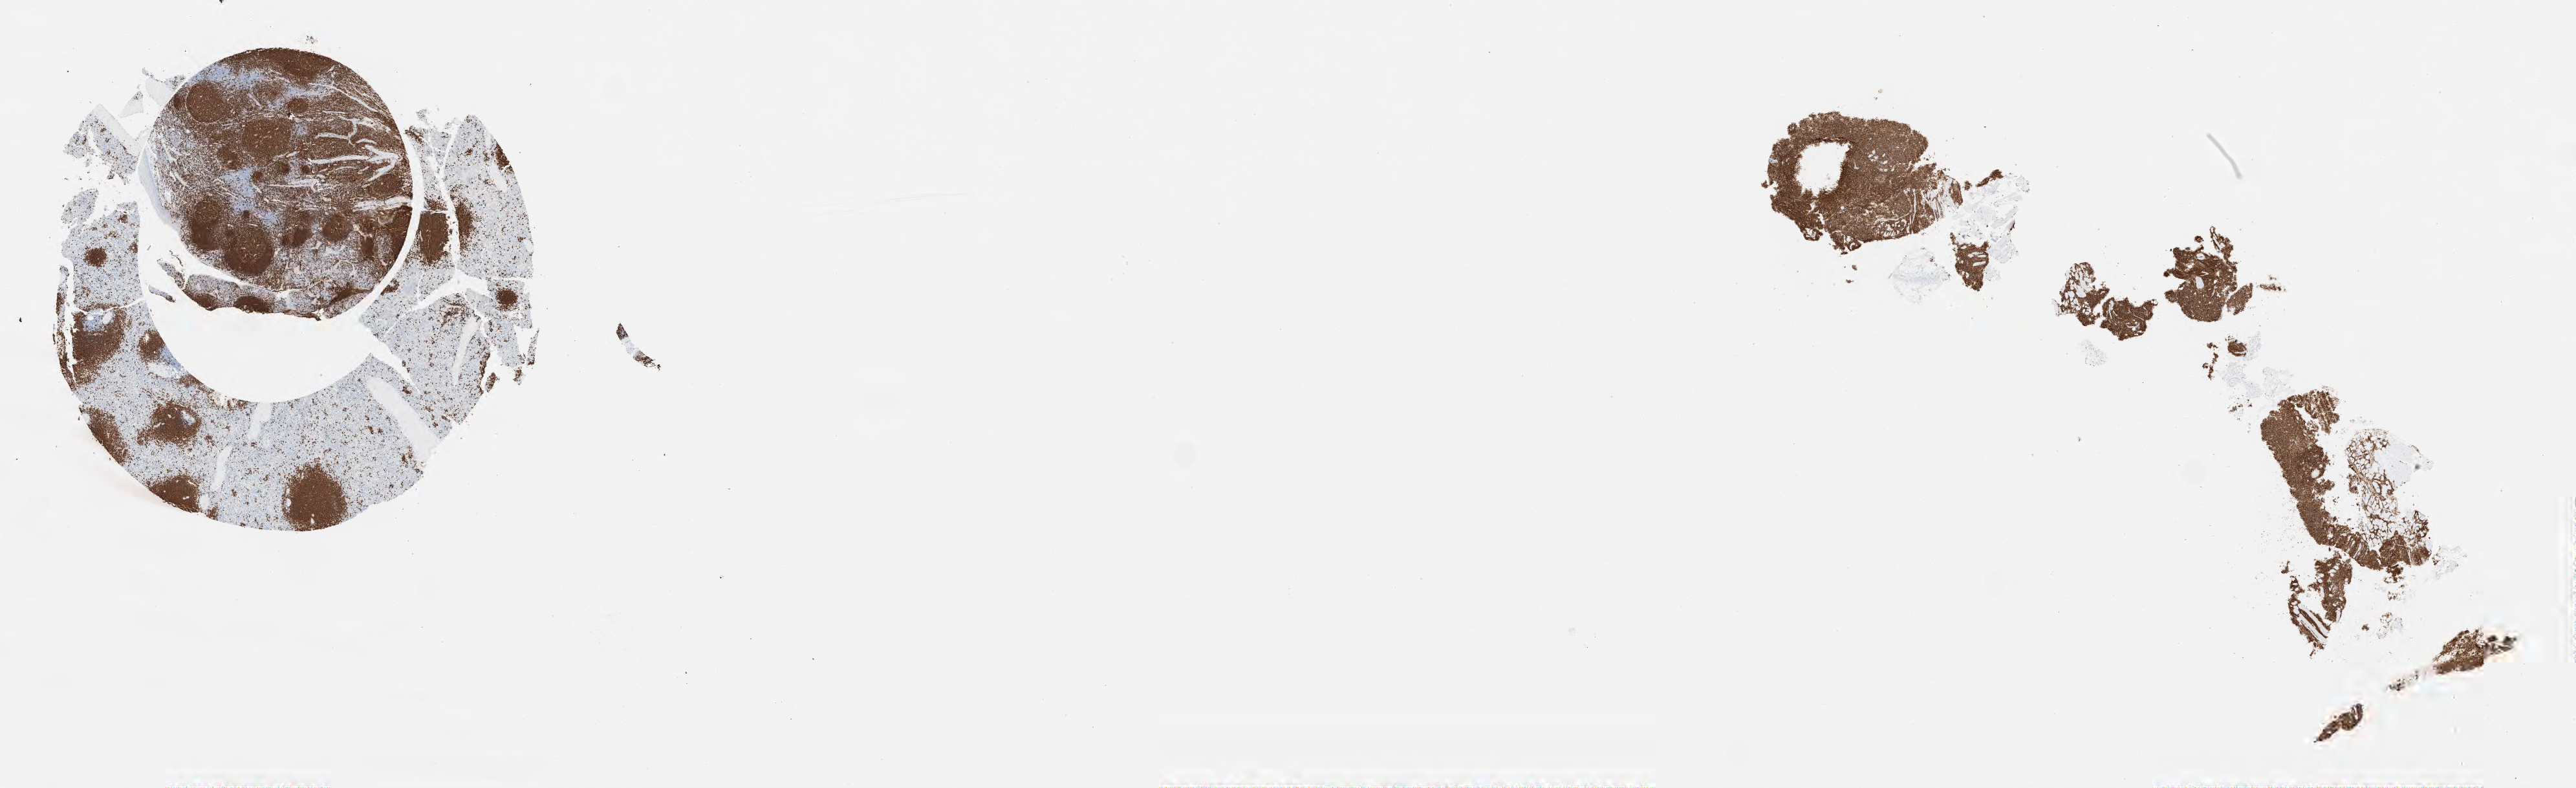
IHC for CD20, whole-slide image, a low-resolution overview of the entire scanned area, about 32.0 x 9.8 mm, specimen: tumor tissue. Patient: female, 69 years old.
- histologic diagnosis: Burkitt lymphoma, NOS